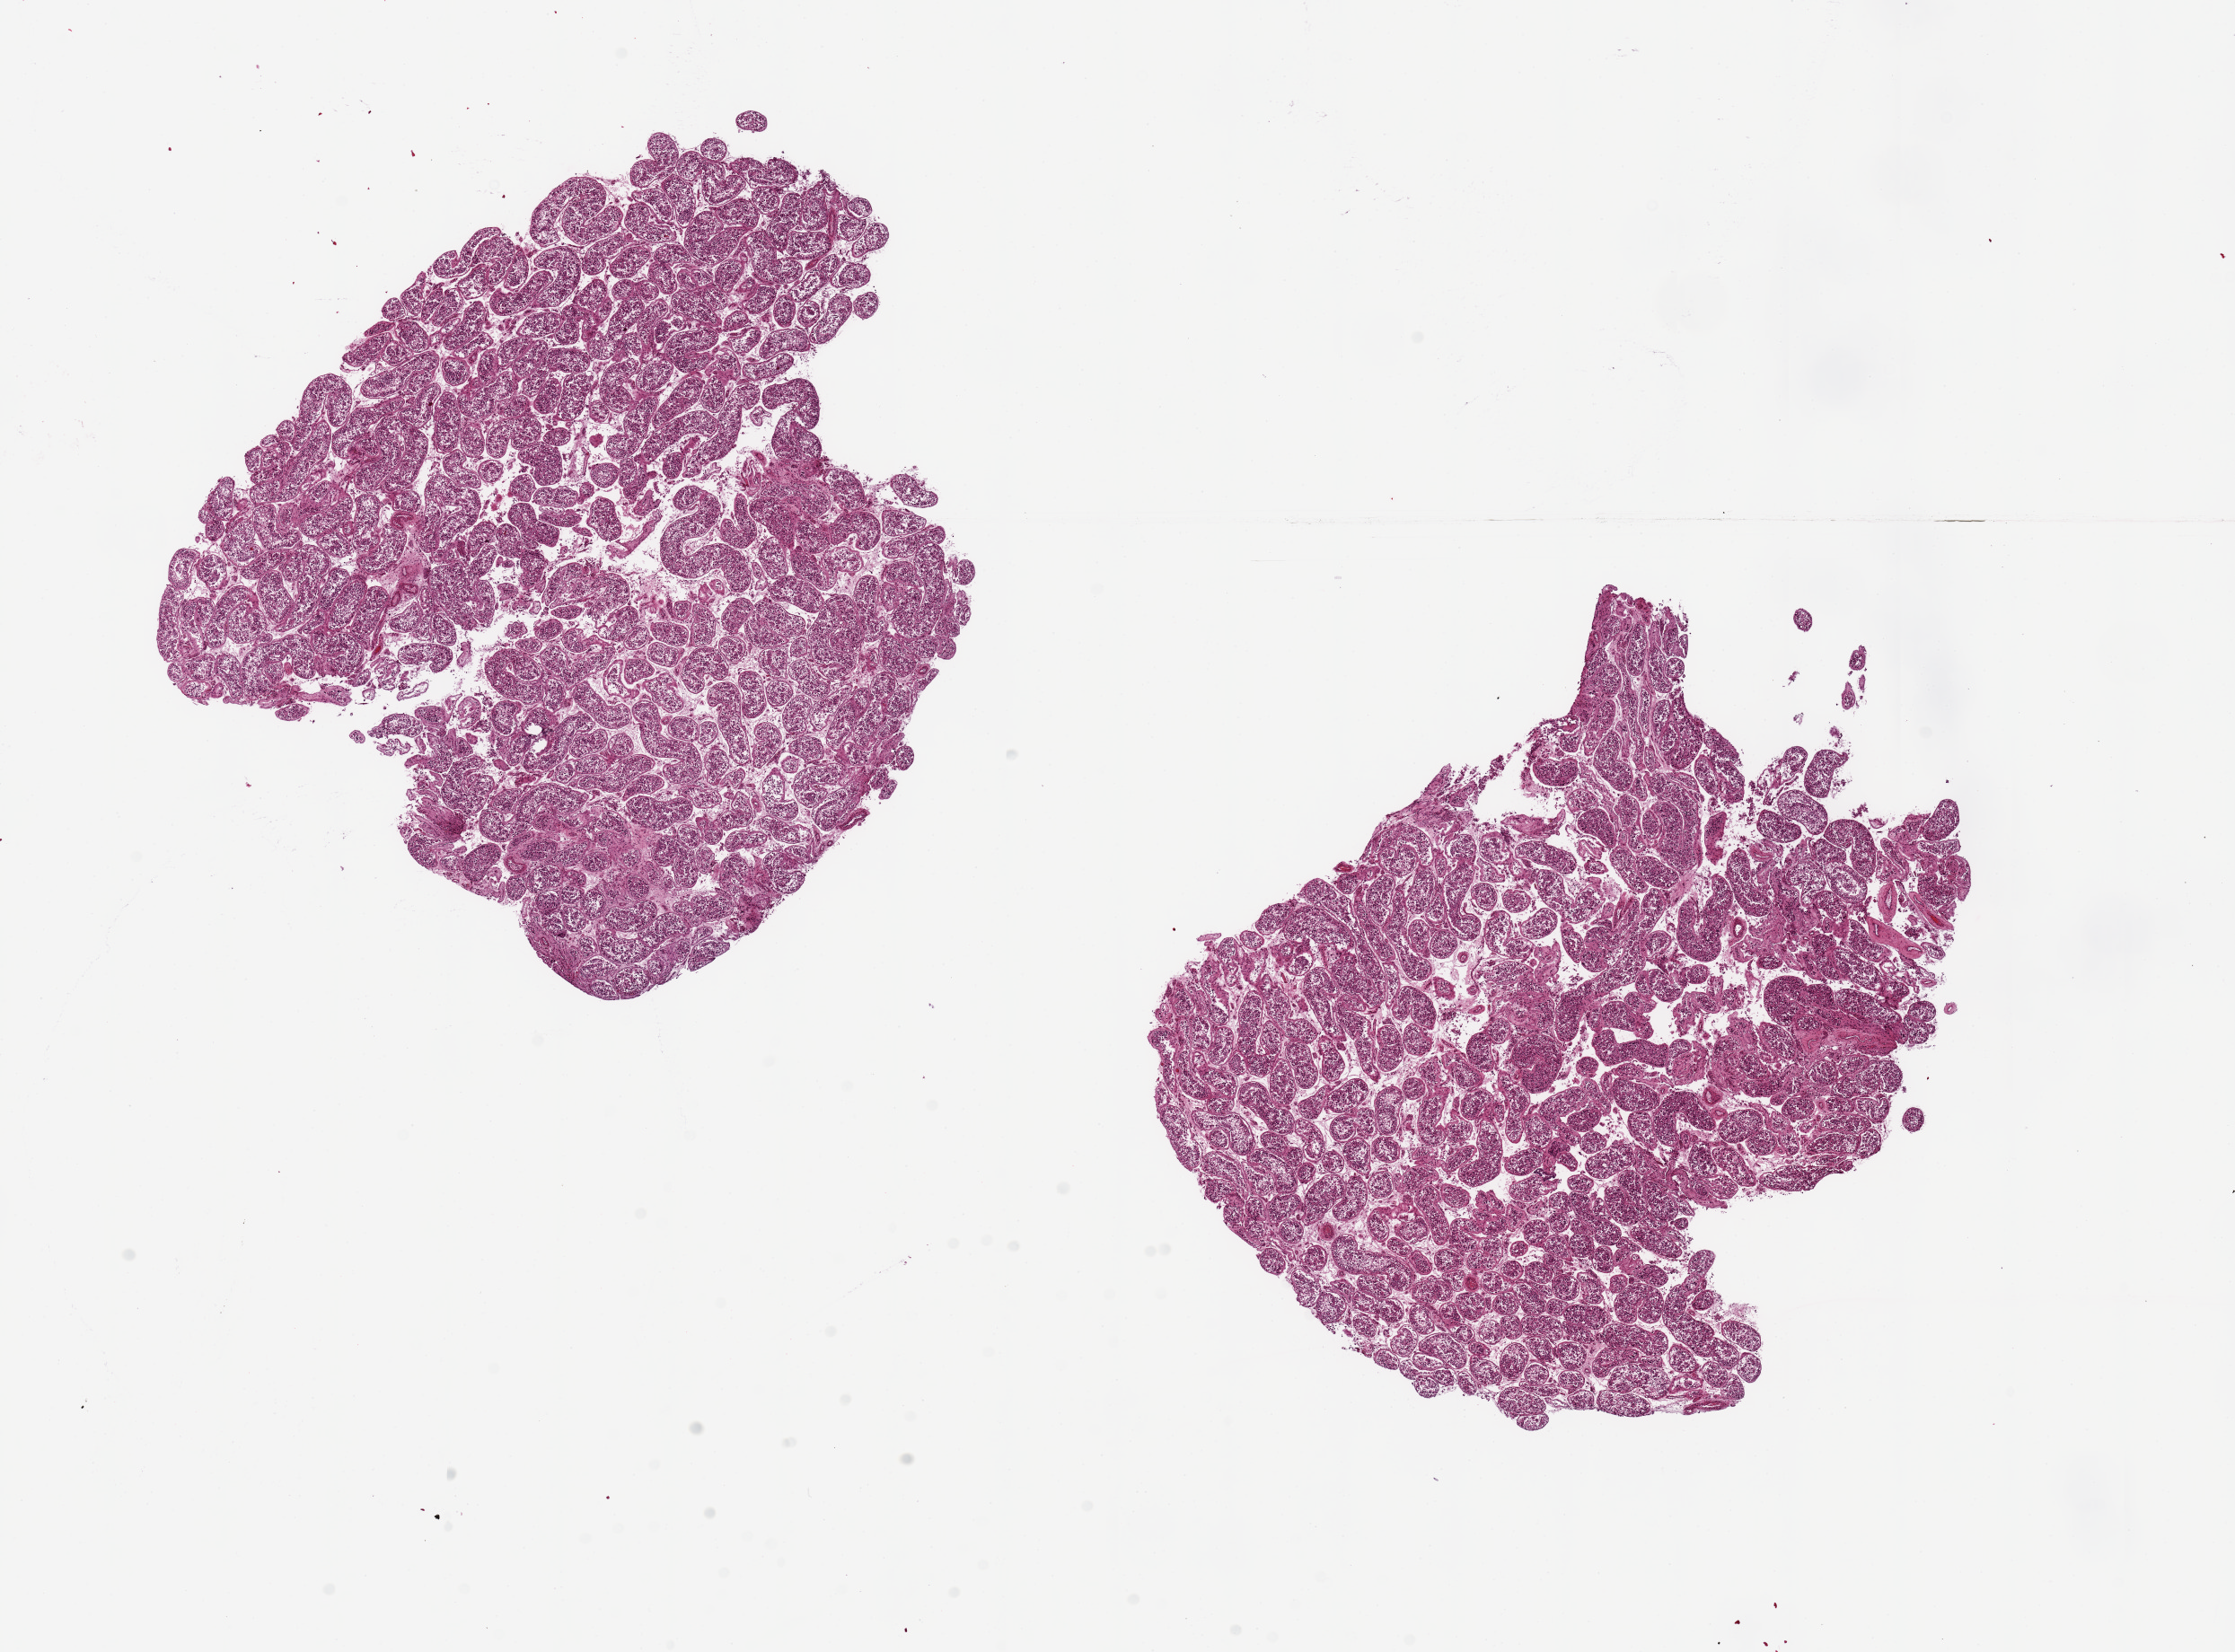
H&E whole-slide image, brightfield — shown as a low-resolution overview of the whole scanned area (about 19.7 x 14.6 mm, from a 20x scan). PAXgene-fixed, paraffin-embedded tissue. Target tissue: testis. Donor tissue sample. Donor sex: male.
• review note (as recorded): 2 pieces, 10x8 & 10x7mm; spermatogenesis present